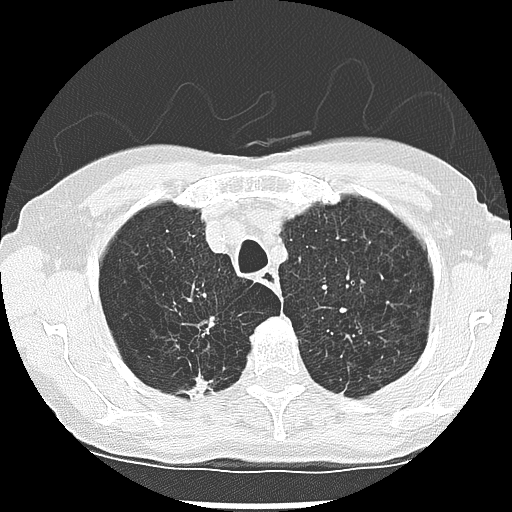
Low-dose screening chest CT, one axial slice; position 222 of 265 along the scan axis; 120 kVp; lung window (W 1500 / L -600 HU); 512 × 512 image matrix, field of view 300 × 300 mm.
Outlined on this slice (manually delineated by an expert):
- lesion 1 (nodule, upper lobe of right lung): bounding box (x1, y1, x2, y2) in pixels: (187, 375, 210, 398)